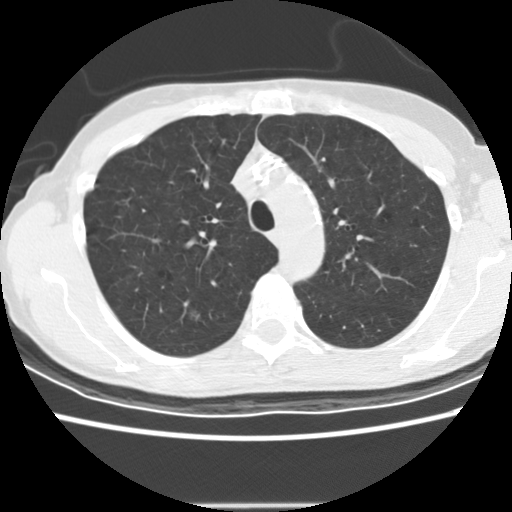
Axial slice from a low-dose chest CT screening exam; second screening round (one year after baseline); lung window (W 1500 / L -600 HU); standard (soft-tissue) reconstruction kernel (STANDARD); slice 41 of 166 in the series. Female participant, aged 58 years at enrolment. Current smoker at enrolment.
Expert-annotated lung lesion, bounding box (x1, y1, x2, y2) in pixels: (172, 299, 212, 329). The screening reader recorded 2 non-calcified nodules or masses ≥4 mm on this exam (right upper lobe, right upper lobe); which of them this box marks is not recorded. Lung cancer was diagnosed 434 days after this screen: bronchiolo-alveolar adenocarcinoma, NOS, right upper lobe, well differentiated (G1), stage IA (AJCC 6th edition), 8 mm at pathology.